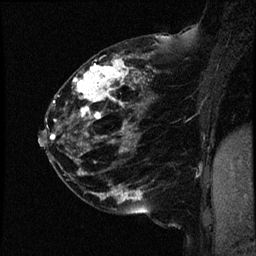
Breast MRI (dynamic contrast-enhanced), one sagittal slice. Slice 24 of 44 in the series (ordered by position). Dynamic contrast-enhanced study with each time point stored as its own series, time point 2 of 4 at this slice position (early post-contrast, ordered by acquisition time). 1.5 T. TE 4.2 ms, TR 17.7 ms. 2 mm slice thickness. 256 × 256 image matrix, field of view 200 × 200 mm. Female patient, age 52 years. From the clinical record (not read from this slice): setting: breast cancer imaged before/during neoadjuvant chemotherapy; receptor status: HR-positive, HER2-negative.
Annotated regions visible in this slice (semi-automatically segmented with operator editing):
- analysis volume of interest (the breast-tissue region the enhancement analysis was run in; not a lesion): bounding box <47,48,163,147> (left, top, right, bottom; pixels)
- tumour enhancement mask (voxels above the 100 % enhancement threshold inside the analysis volume of interest): <51,56,144,145>